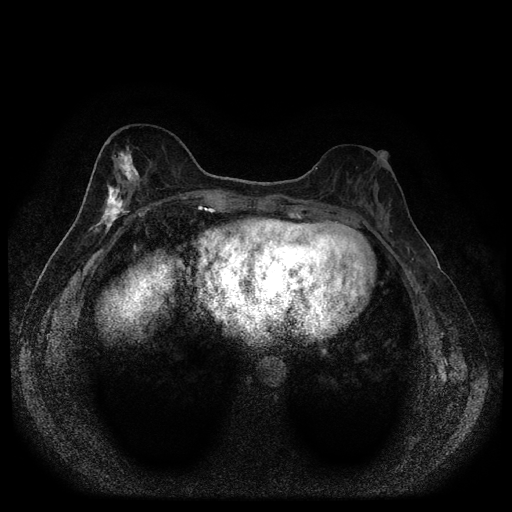
Breast MRI (dynamic contrast-enhanced, multi-phase), one axial slice; slice 39 of 116 in the series (ordered by position); dynamic contrast-enhanced series, time point 2 of 5 at this slice position (early post-contrast); 1.5 T; TE 2.7 ms, TR 5.4 ms; 512 × 512 image matrix, field of view 330 × 330 mm. Female patient, age 49 years.
Structures marked on this image (semi-automatic segmentation, software-assisted and operator-edited):
- breast lesion (labelled 'tumour' in the annotation; benign lesions carry a separate 'benign' label): bounding box <82,144,143,246> (left, top, right, bottom; pixels)